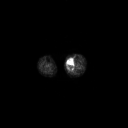
FDG PET of an extremity soft-tissue mass (from a PET/CT study), one axial slice. Slice 133 of 223 in the series (ordered by position). 3.27 mm slice thickness. 128 × 128 image matrix, field of view 700 × 700 mm. Female patient, age 70 years. Case-level facts recorded for this patient, not image findings: histological type: extraskeletal high grade osteogenic sarcoma; grade: high; site of the primary tumour: left calf.
Annotated regions visible in this slice (expert contour drawn on MRI and transferred to this co-registered scan by the dataset authors):
- gross tumour volume (mass): bounding box (x1, y1, x2, y2) in pixels: (67, 60, 74, 69)